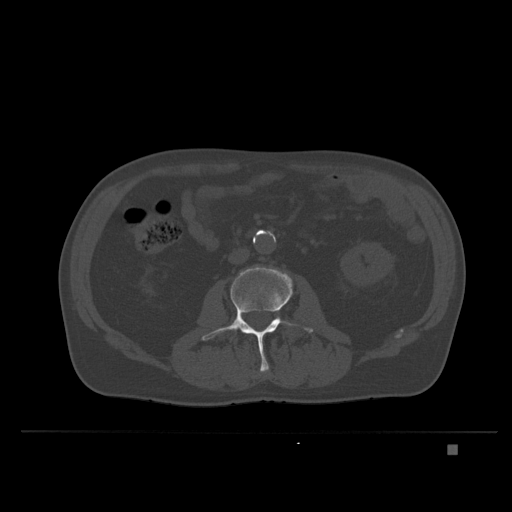
CT including the spine, one axial slice. Slice 97 of 435 in the series (ordered by position). Bone window (W 1800 / L 400 HU). 512 × 512 image matrix. Patient: male, 73 years. Case-level facts recorded for this patient, not image findings: primary cancer: skin.
Structures marked on this image (semi-automatic segmentation, software-assisted and operator-edited):
- L2 vertebra: box from (x=255, y=369) to (x=268, y=377) px
- L3 vertebra: (x=201, y=265)–(x=313, y=371)